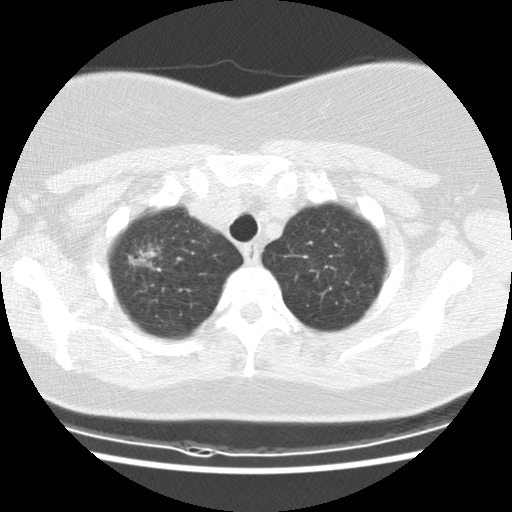
Low-dose screening chest CT, one axial slice; slice 116 of 132 in the series (ordered by position); reconstruction kernel STANDARD; 120 kVp; lung window (W 1500 / L -600 HU); 512 × 512 image matrix, field of view 326 × 326 mm.
Annotated regions visible in this slice (expert manual segmentation):
- lesion 1 (tumor, upper lobe of right lung): bounding box <128,244,160,270> (left, top, right, bottom; pixels)